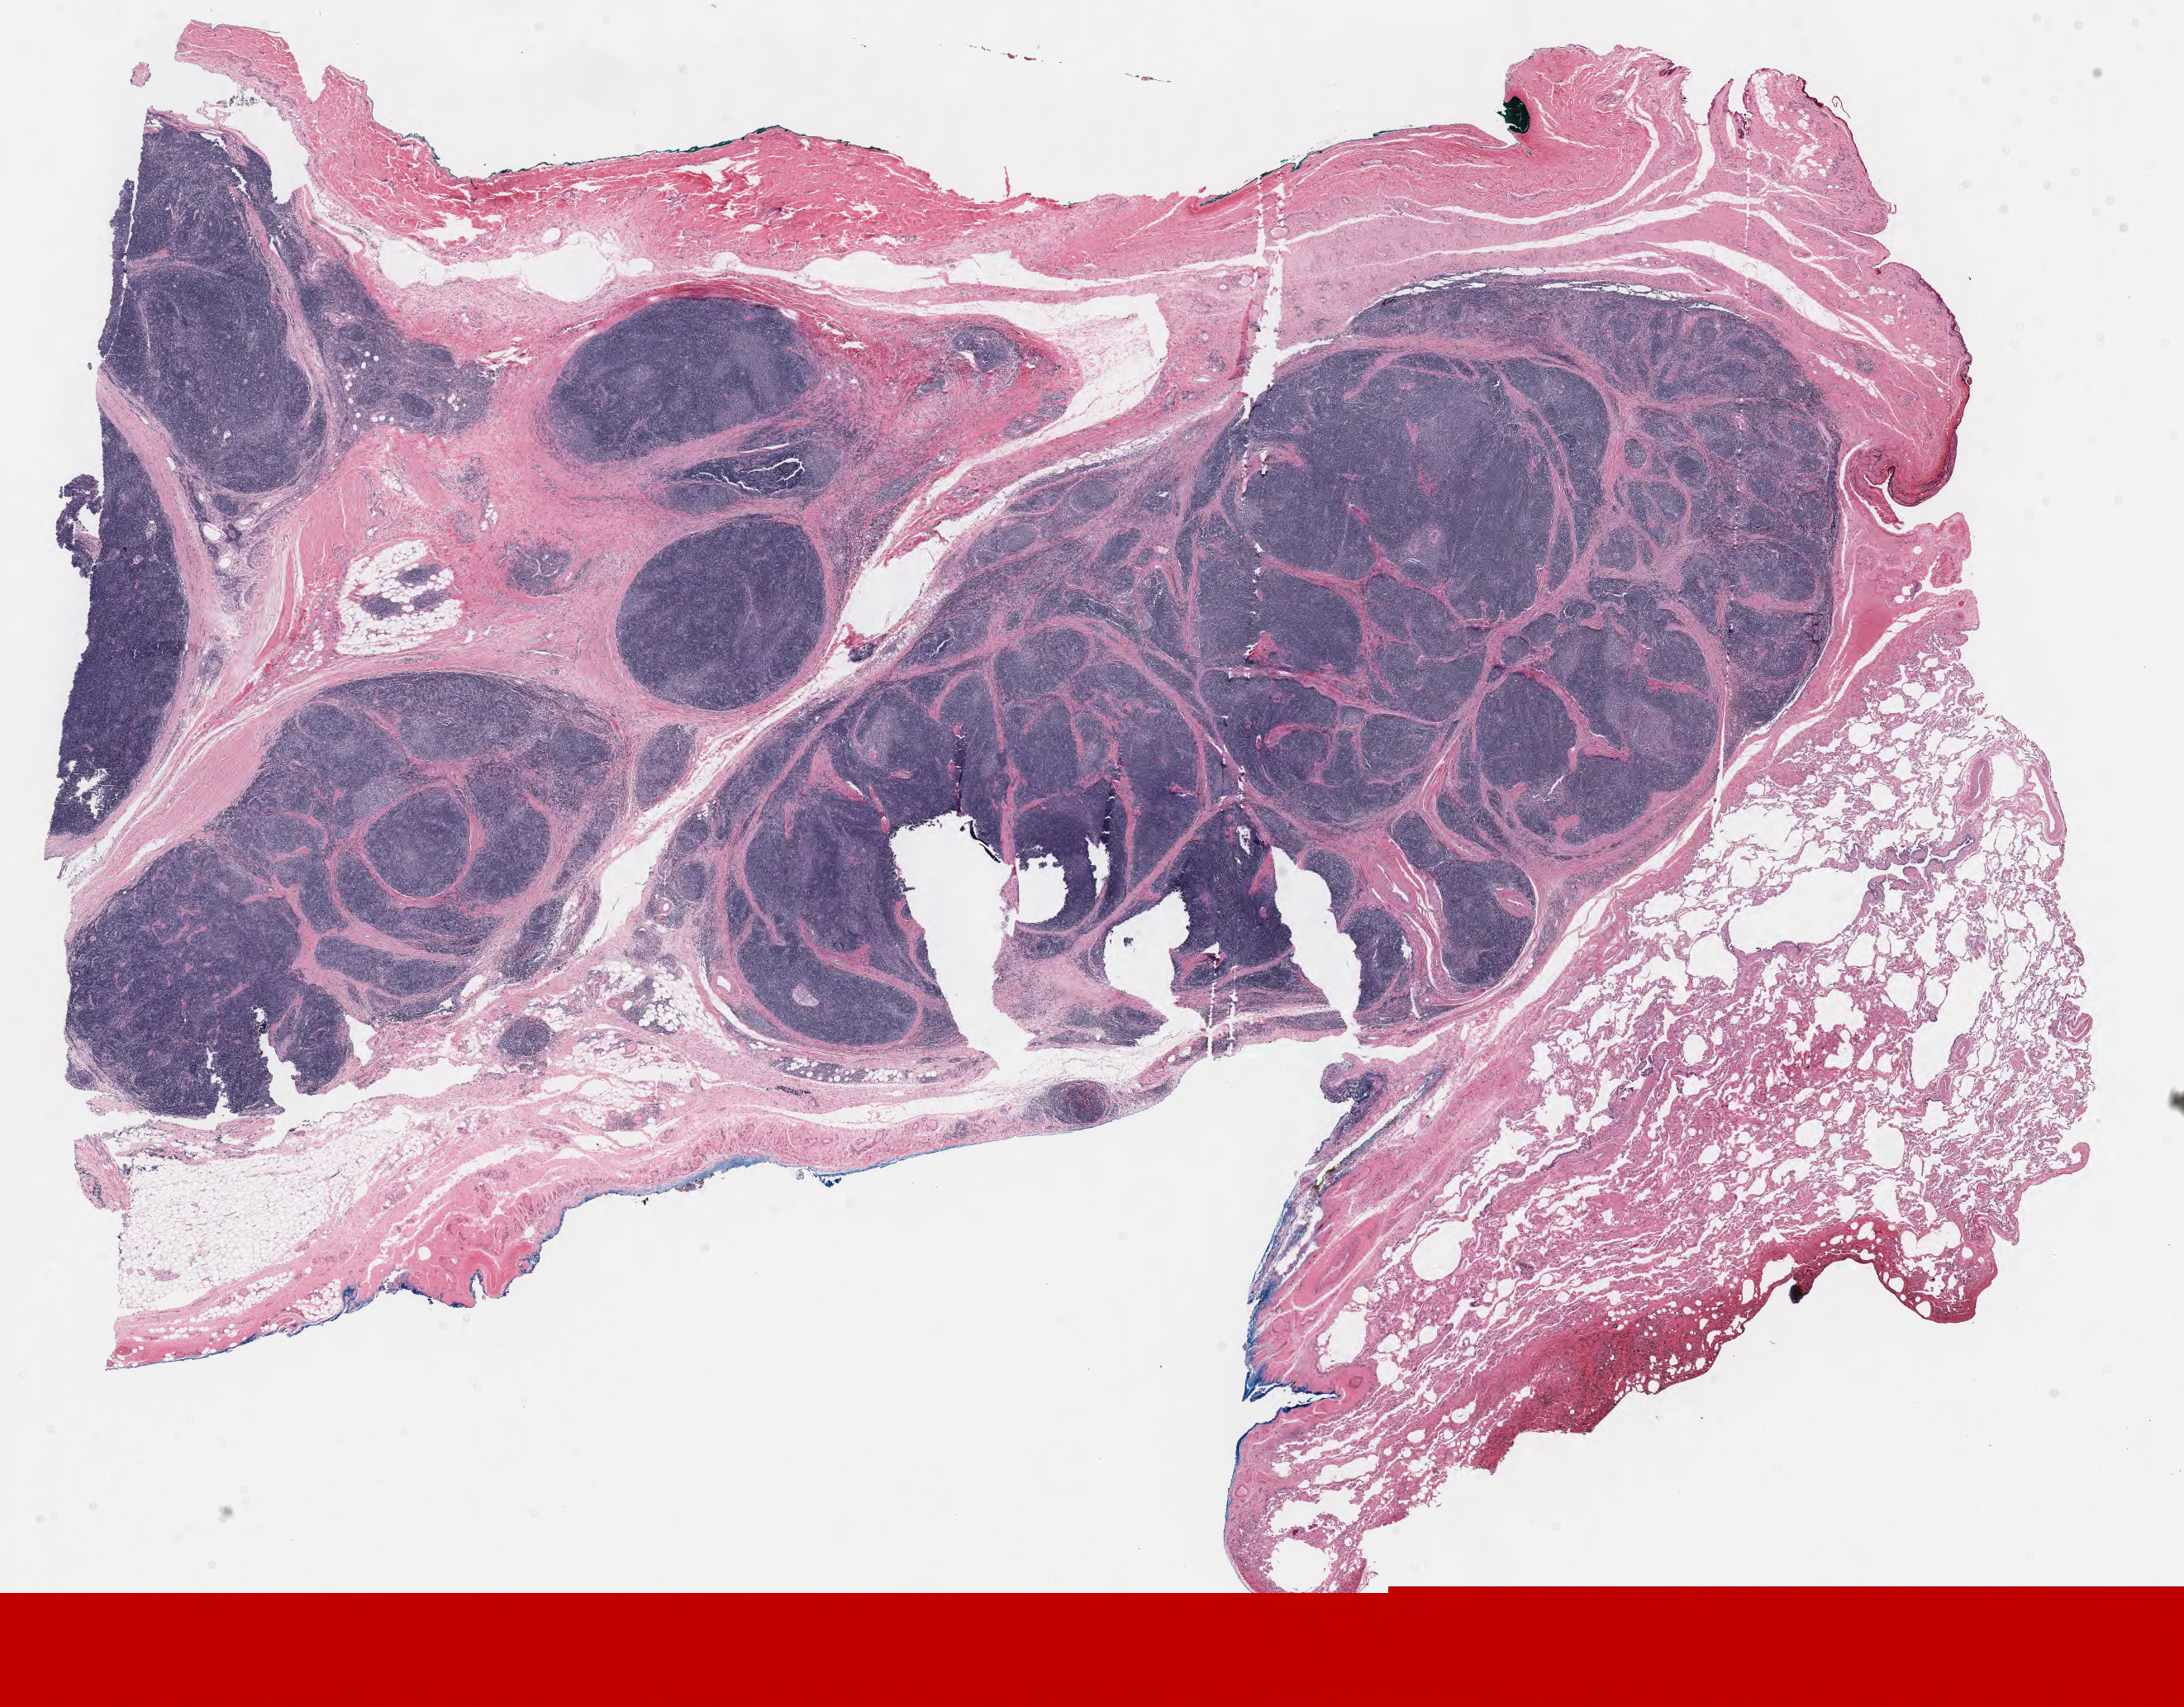
H&E whole-slide image, low-resolution overview of the scanned area, about 42.3 x 33.1 mm, FFPE section, primary tumour sample from the thymus. Patient: female, age at initial diagnosis 57 years.
Diagnosis: Thymoma, type B1, NOS.